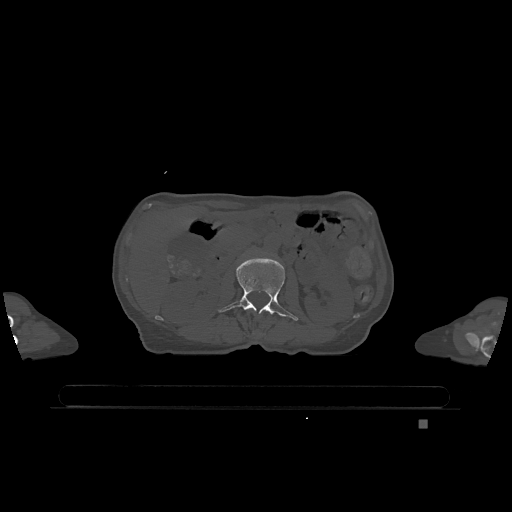
CT including the spine, one axial slice; position 417 of 1317 along the scan axis; bone window (W 1800 / L 400 HU); 0.5 mm slice thickness; 512 × 512 image matrix, field of view 500 × 500 mm. Female patient, age 74 years. From the clinical record (not read from this slice): primary cancer: lung.
Structures marked on this image (semi-automatically segmented with operator editing):
- L2 vertebra: bounding box <218,257,298,321> (left, top, right, bottom; pixels)